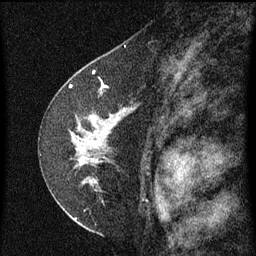
Breast MRI (dynamic contrast-enhanced), one sagittal slice; slice 40 of 60 in the series (ordered by position); dynamic contrast-enhanced series, image 2 of 3 at this slice position (ordered by acquisition); 1.5 T; TE 4.2 ms, TR 8 ms; 256 × 256 image matrix, field of view 180 × 180 mm. Patient: female, 47 years.
Structures marked on this image (semi-automatically segmented with operator editing):
- analysis volume of interest (the breast-tissue region the enhancement analysis was run in; not a lesion): bounding box (x1, y1, x2, y2) in pixels: (44, 84, 143, 199)
- tumour enhancement mask (voxels above the 70 % enhancement threshold inside the analysis volume of interest): (70, 86, 125, 183)